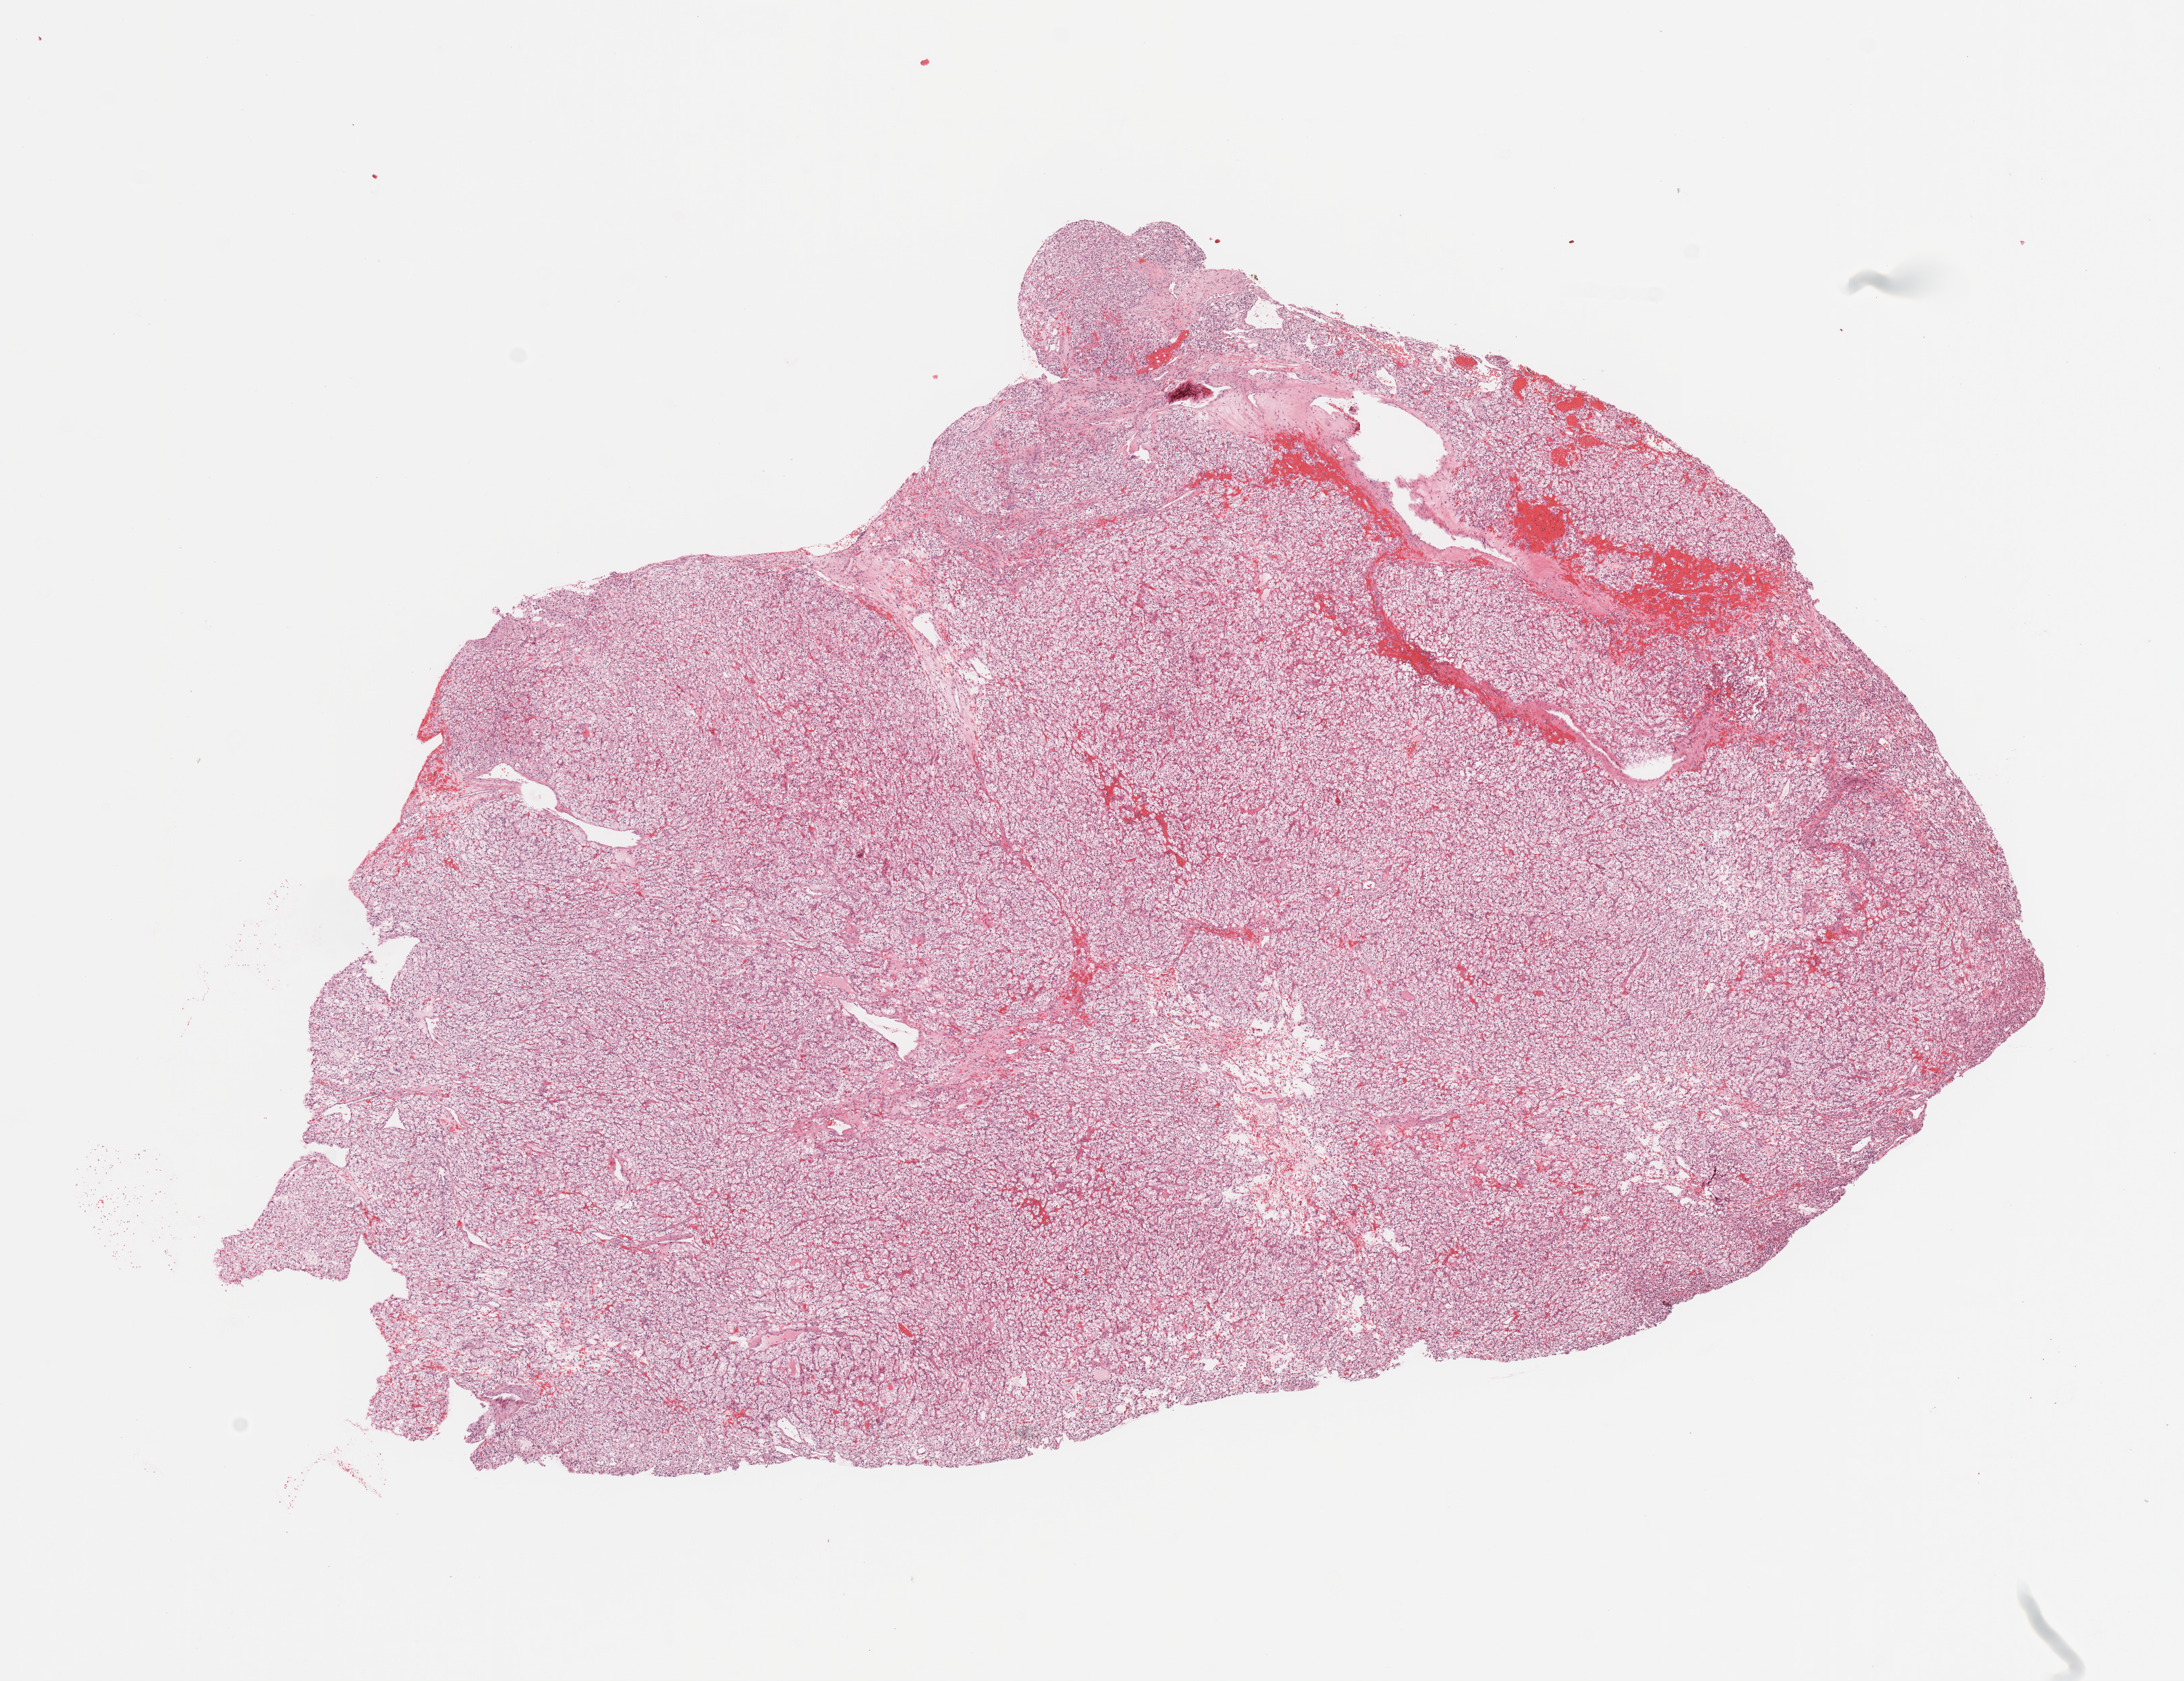
H&E whole-slide image, shown as a low-resolution overview of the whole scanned area (about 12.8 x 9.8 mm, from a 20x scan); tumour tissue sample, sampled site: kidney. Patient: female, age 68 years. Histologic grade: G4 (undifferentiated). Composition of this section per pathologist review: tumour nuclei 90%, necrosis 3%.
• diagnosis: Renal cell carcinoma, NOS
• AJCC pathologic stage: I
• primary tumour site (as recorded): lower pole